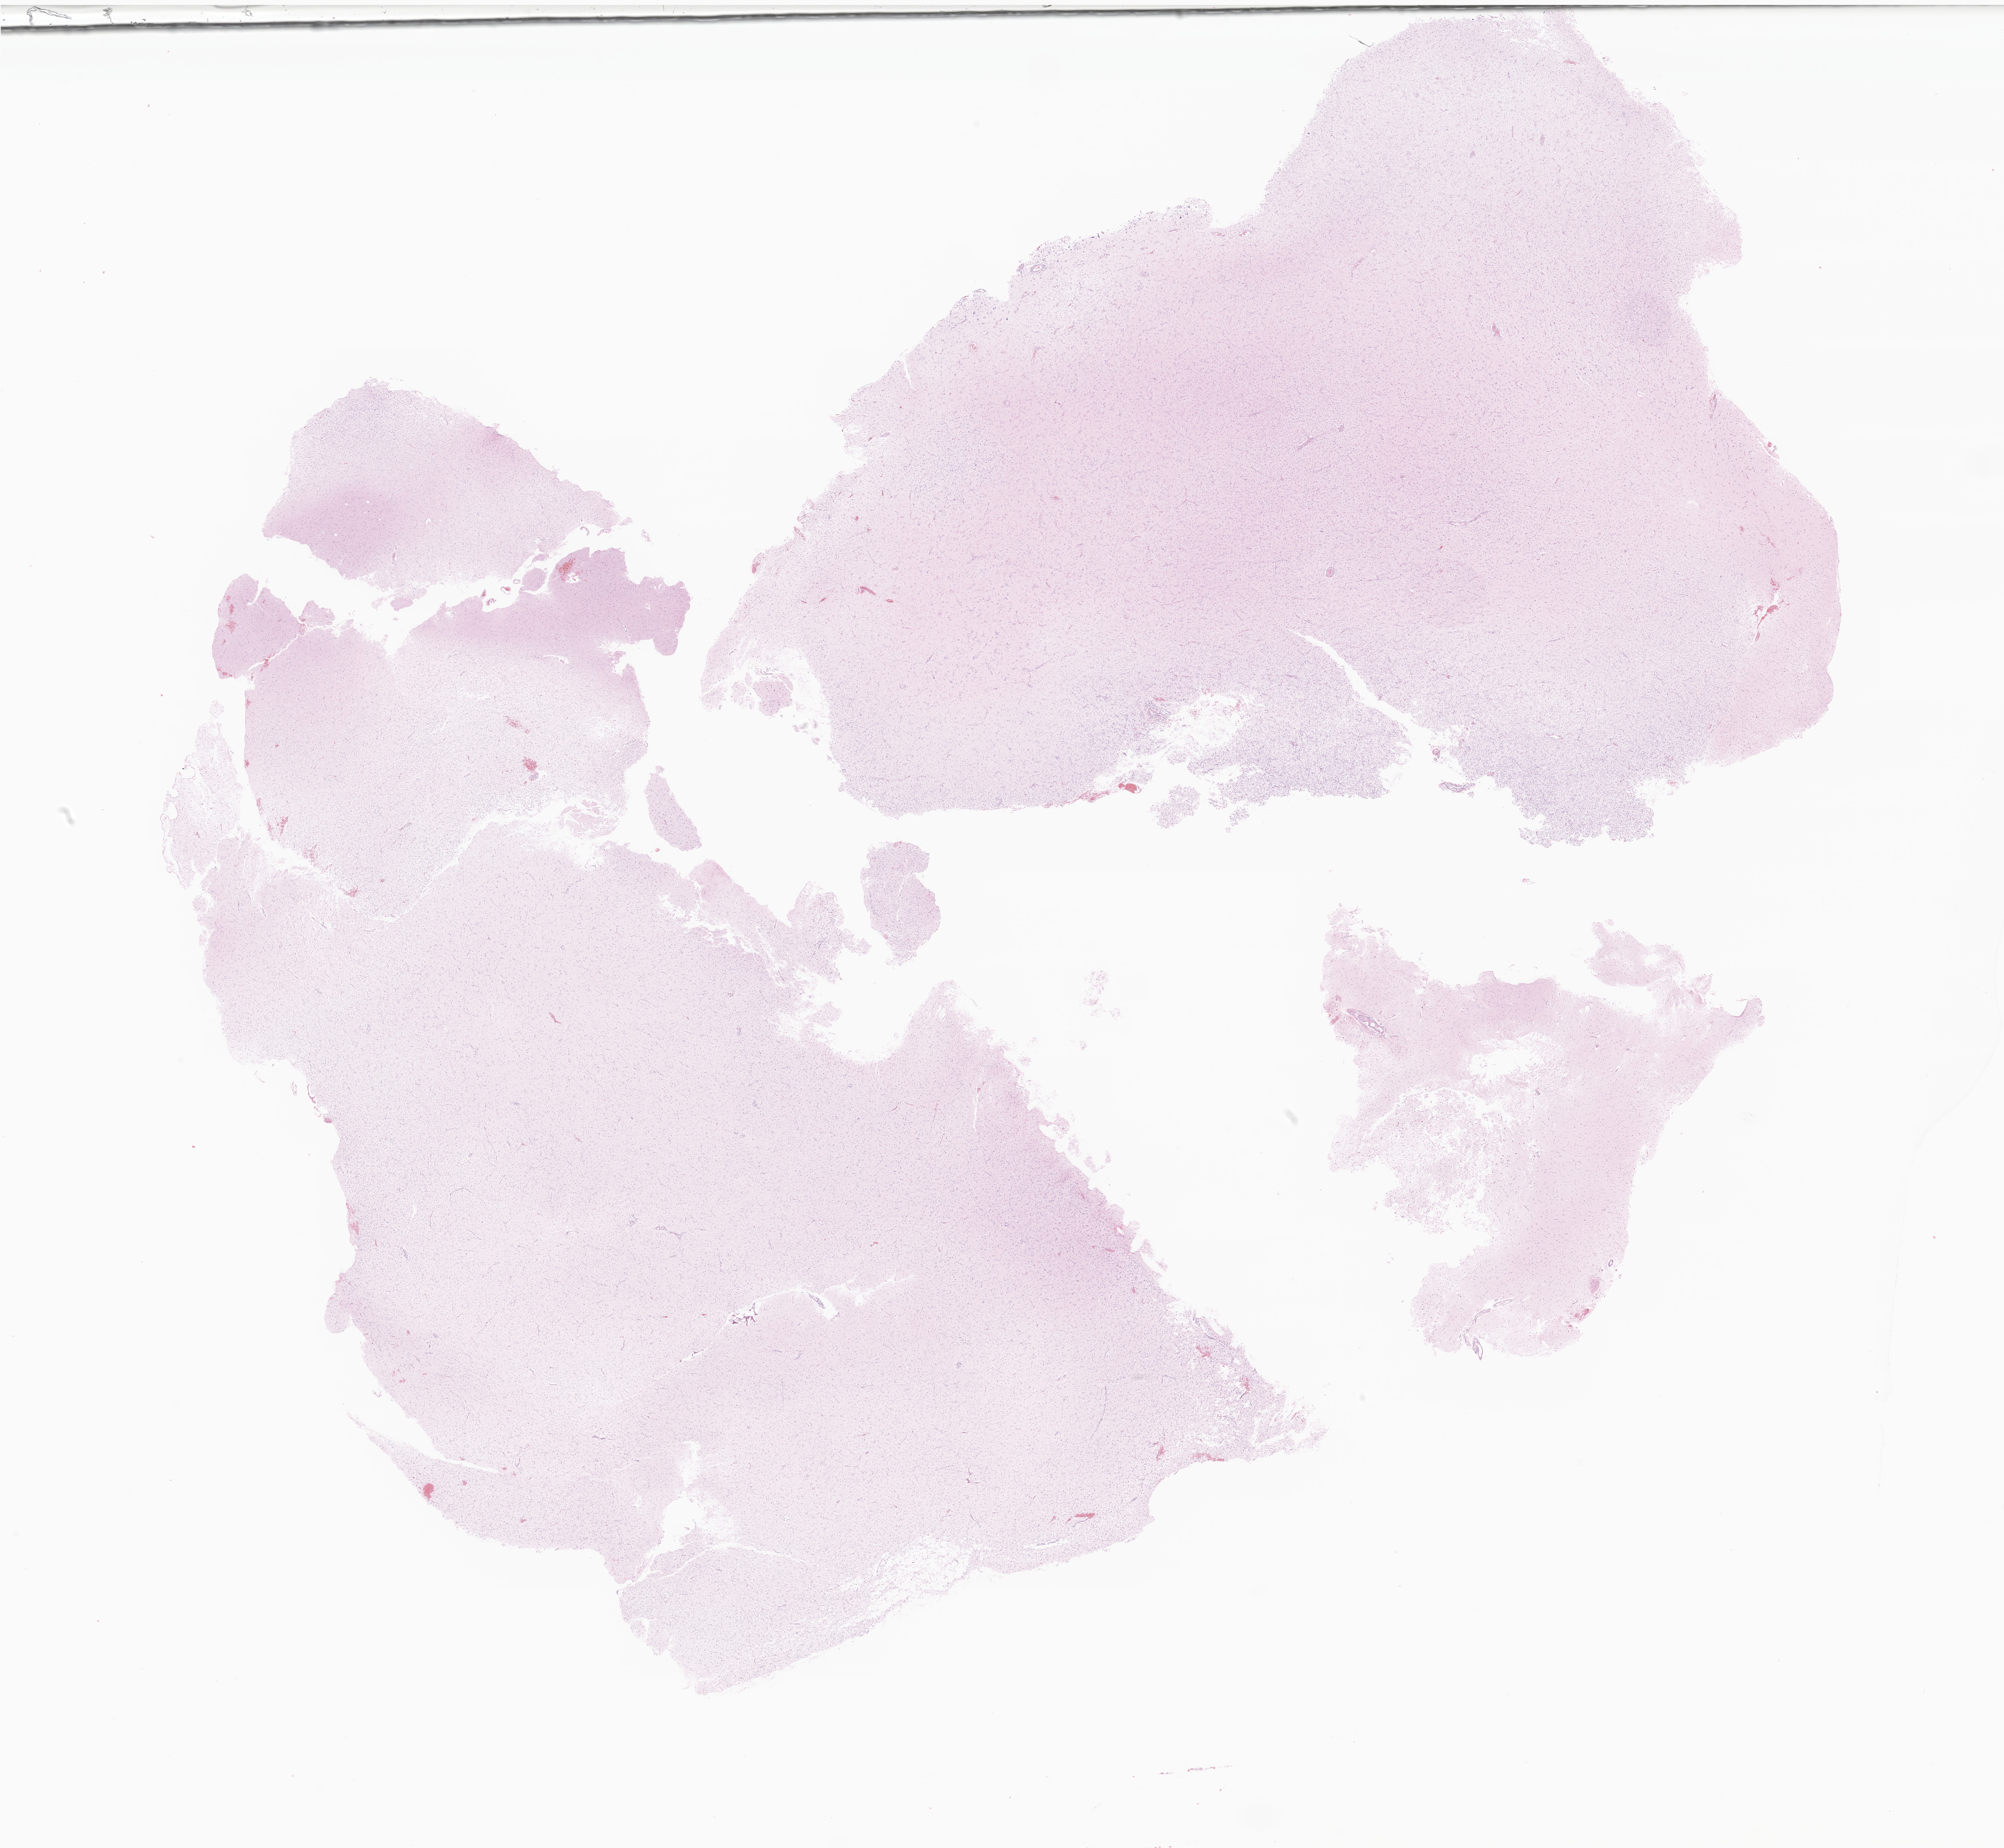
Whole-slide image, haematoxylin and eosin stain of tumor tissue from the parietal lobe, shown as a low-resolution overview of the whole scanned area (about 24.1 x 22.3 mm), formalin-fixed, paraffin-embedded (FFPE) tissue. Male patient, age 156 months.
Diagnosis: Dysembryoplastic neuroepithelial tumor.